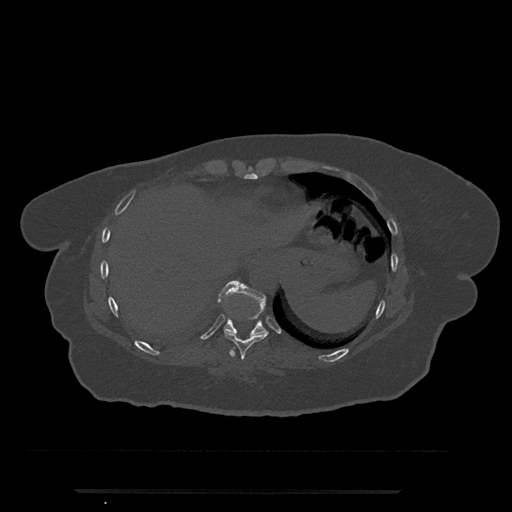
CT including the spine, one axial slice; slice 318 of 797 in the series (ordered by position); reconstruction kernel Br40s/3; 120 kVp; bone window (W 1800 / L 400 HU); 512 × 512 image matrix, field of view 440 × 440 mm. Patient: female, 51 years. From the clinical record (not read from this slice): primary cancer: neuro.
Outlined on this slice (semi-automatic segmentation, software-assisted and operator-edited):
- T10 vertebra: bounding box [x1, y1, x2, y2] px = [218, 280, 266, 336]
- T9 vertebra: [224, 330, 268, 360]